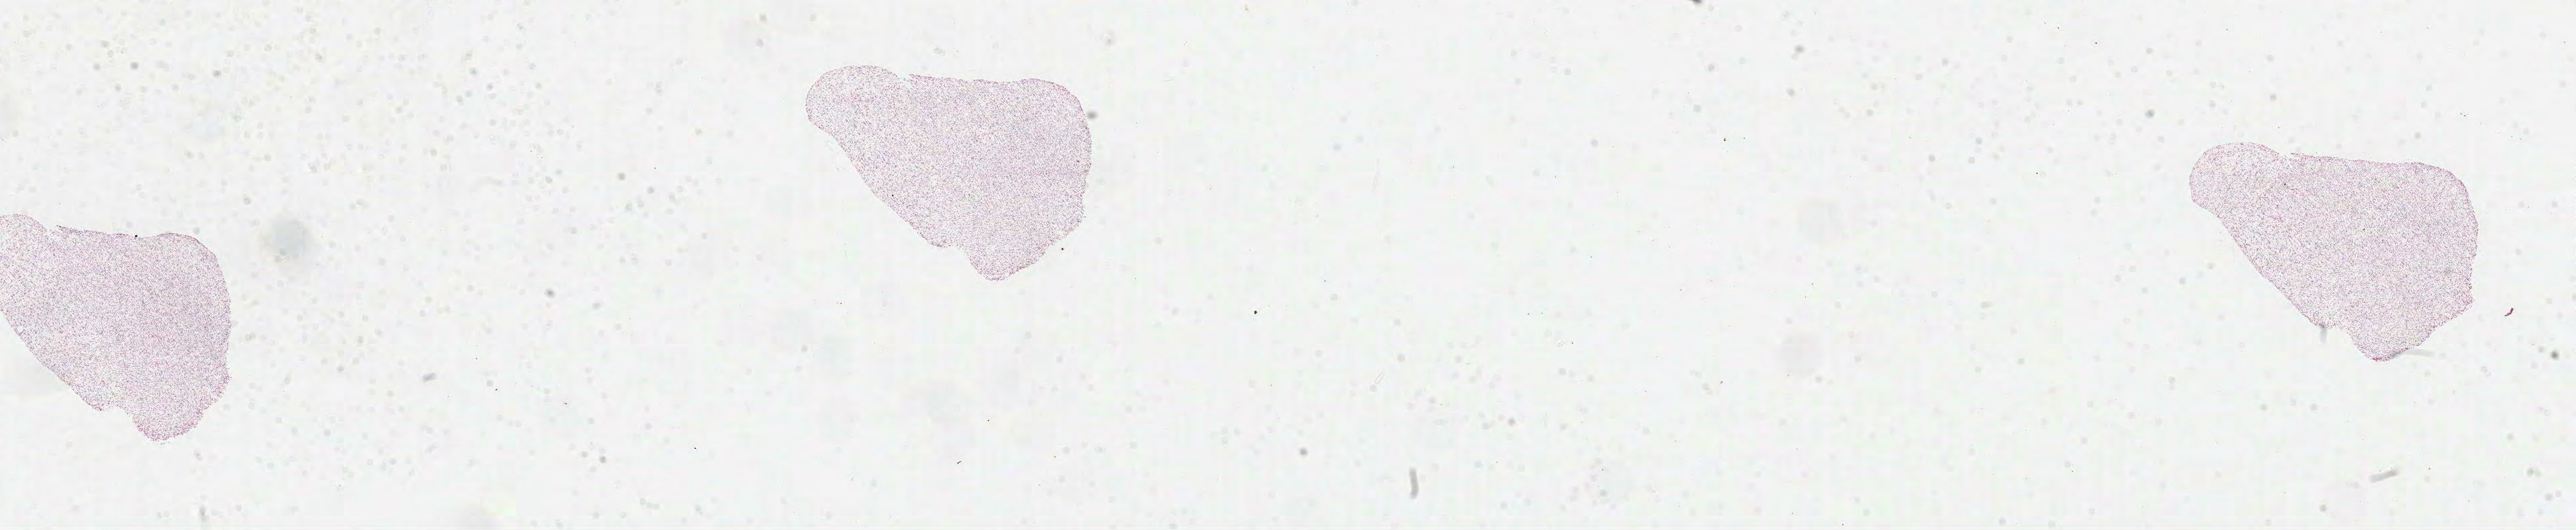
Digitized Hematoxylin and eosin (H&E) stained tissue section (whole slide) — low-resolution overview of the scanned area, about 30.9 x 6.4 mm (acquisition: 40x scan), formalin-fixed paraffin-embedded (FFPE) diagnostic section, primary tumour sample from the brain. Patient: female, age at initial diagnosis 82 years.
* diagnosis: Glioblastoma